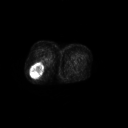
FDG PET of an extremity soft-tissue mass (from a PET/CT study), one axial slice; slice 35 of 267 in the series (ordered by position); 128 × 128 image matrix, field of view 700 × 700 mm. Patient: female, 70 years. From the clinical record (not read from this slice): histological type: synovial sarcoma; grade: intermediate; site of the primary tumour: right buttock.
Annotated regions visible in this slice (expert contour drawn on MRI and transferred to this co-registered scan by the dataset authors):
- gross tumour volume including surrounding oedema: box from (x=30, y=61) to (x=43, y=78) px
- gross tumour volume (mass): (x=30, y=62)–(x=43, y=78)